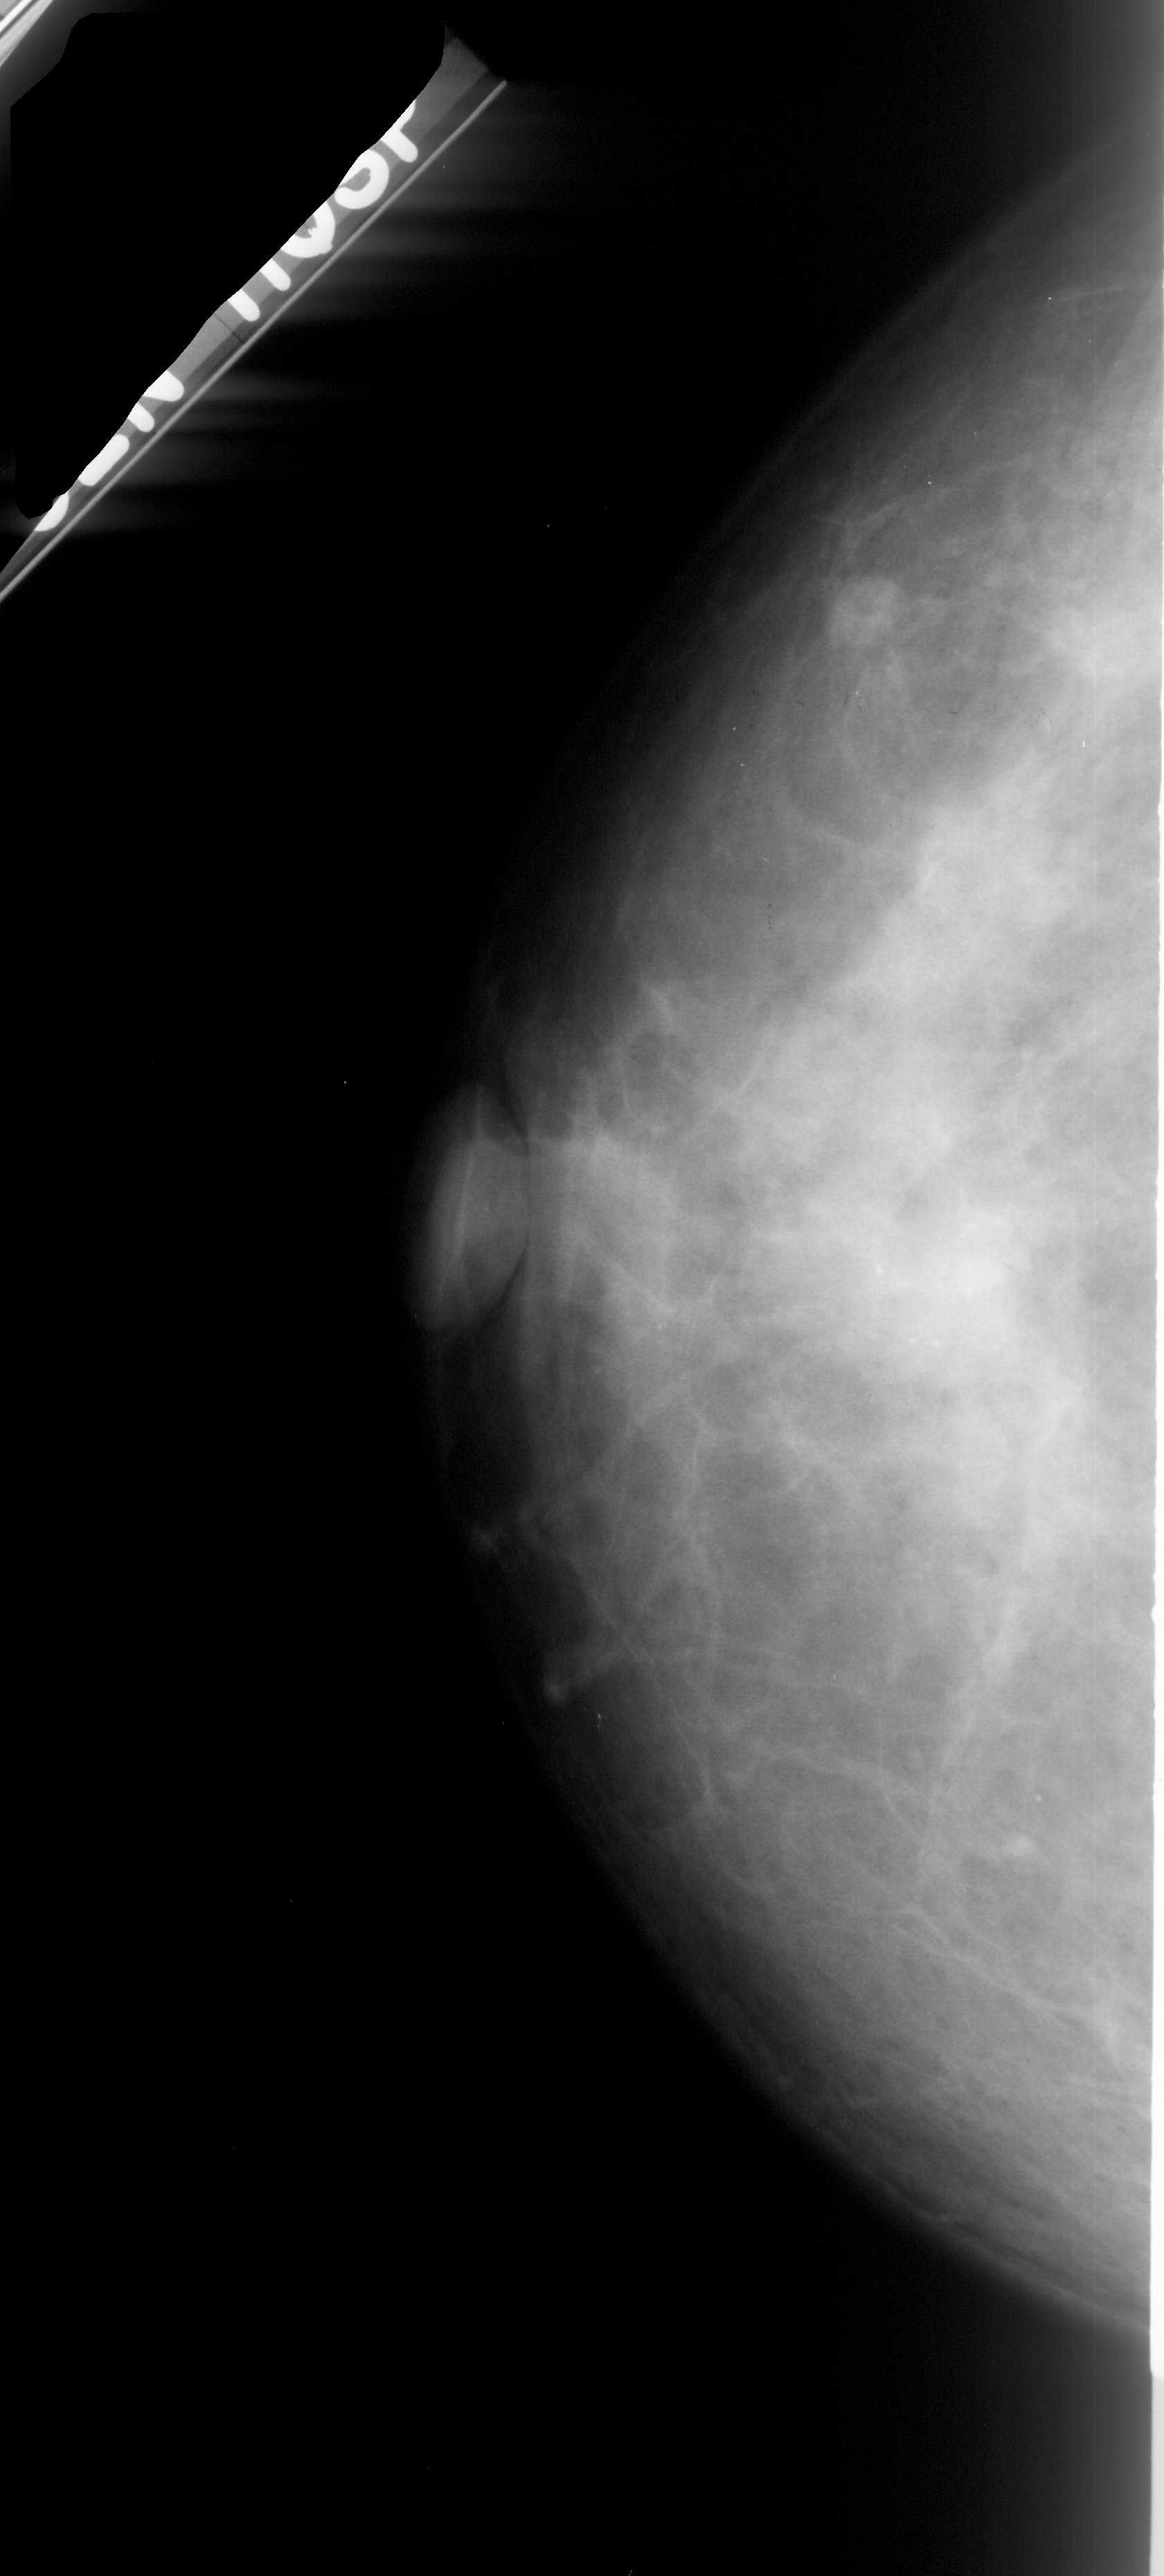
Digitized screen-film mammogram. Left breast. Craniocaudal (CC) view. 1164 × 2576 image matrix.
Expert-marked regions of interest on this image (one box per marked abnormality):
- calcifications, morphology pleomorphic, distribution clustered; BI-RADS assessment category 4; pathology (as recorded): malignant: bounding box (x1, y1, x2, y2) in pixels: (797, 1212, 1038, 1439)